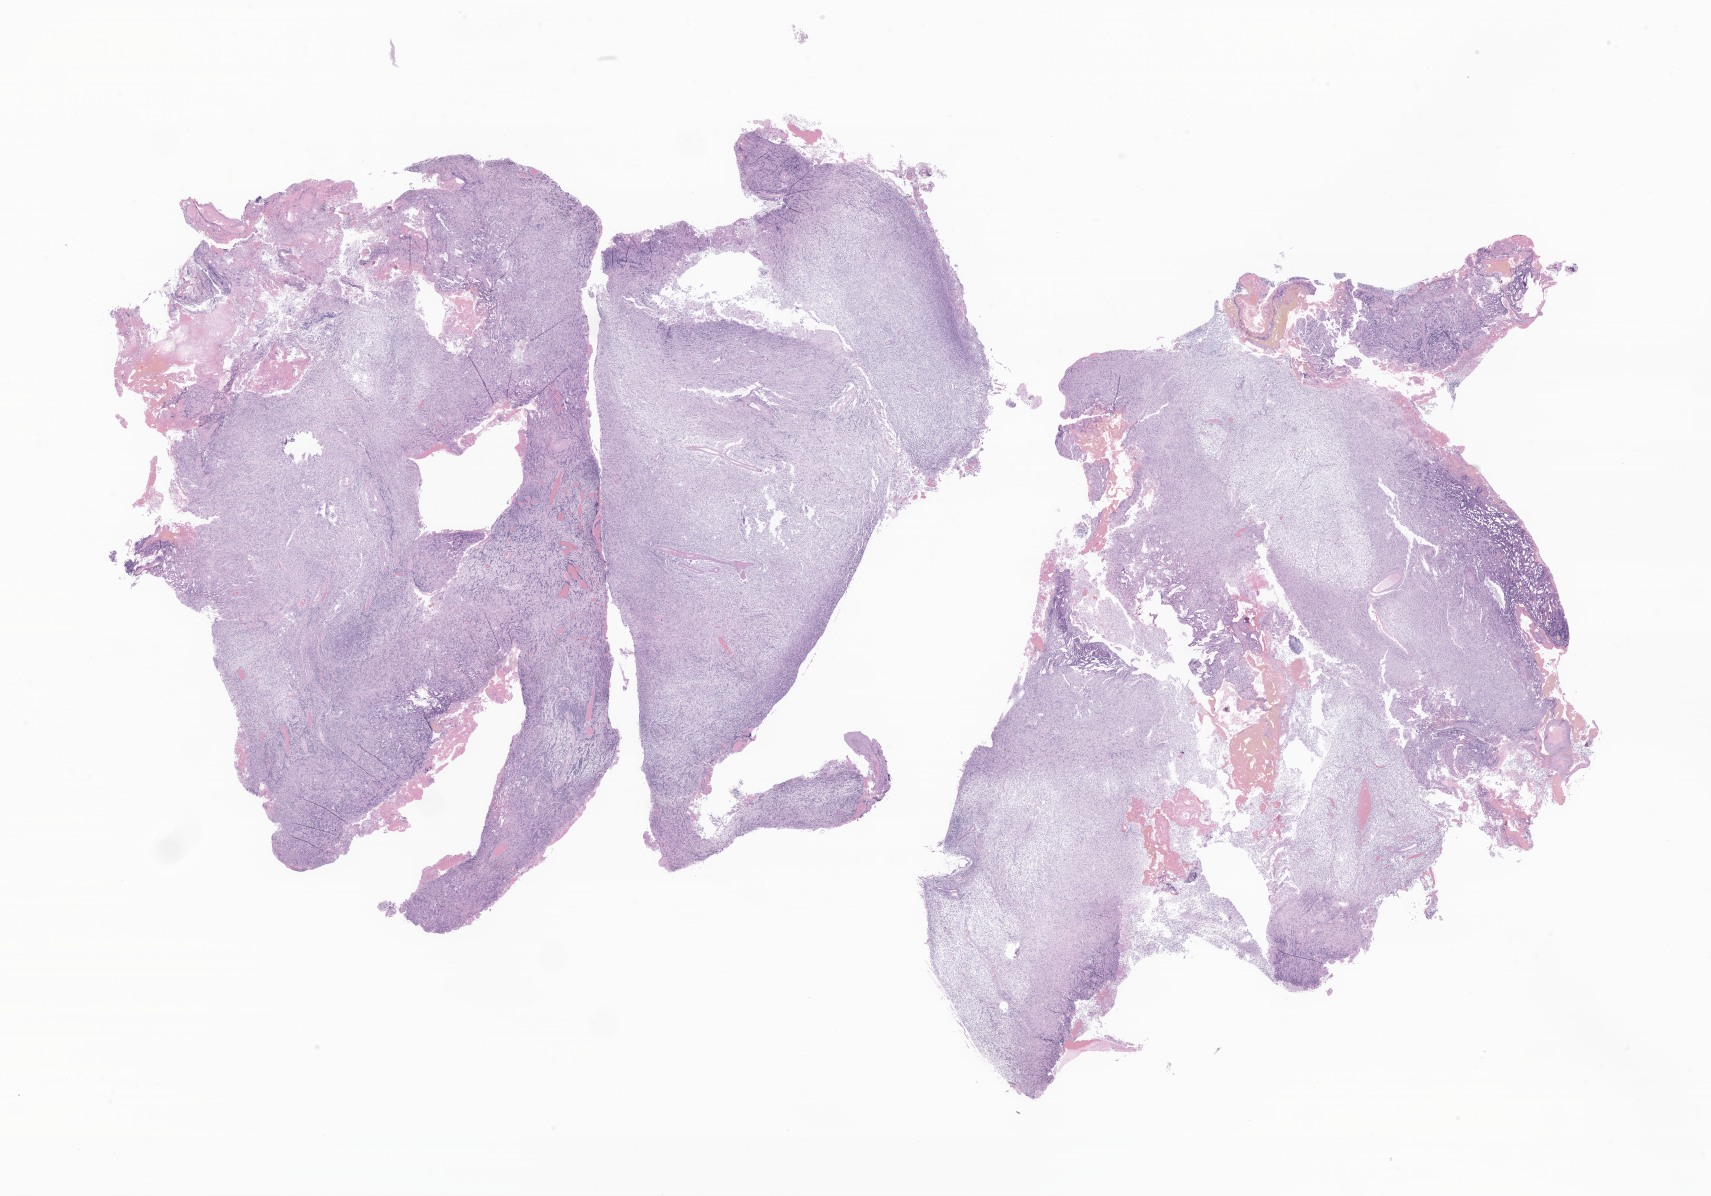
Haematoxylin and eosin whole-slide image of tumor tissue from the brain, low-resolution overview of the scanned area, about 28.9 x 20.2 mm, formalin-fixed, paraffin-embedded (FFPE) tissue. Patient female; age 72 months.
- recorded diagnosis: Medulloblastoma, NOS